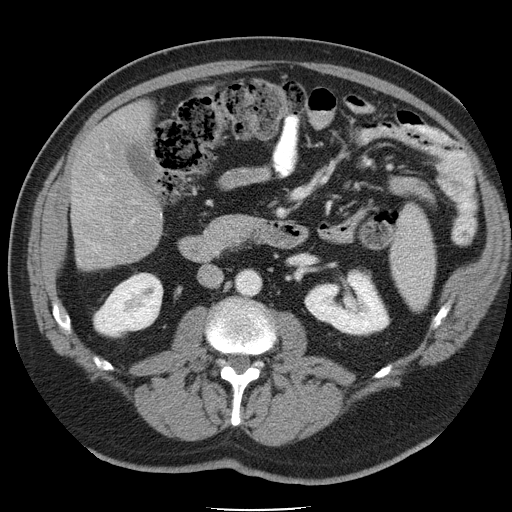
Contrast-enhanced abdominal CT, one axial slice. Slice 14 of 45 in the series (ordered by position). 120 kVp. Intravenous contrast given. Soft-tissue window (W 400 / L 40 HU). 5 mm slice thickness. 512 × 512 image matrix, field of view 386 × 386 mm. Male patient, age 65 years. Case-level facts recorded for this patient, not image findings: diagnosis: colorectal cancer liver metastases, imaged before liver resection; multiple liver metastases: yes; largest metastasis: 4.9 cm; disease in both lobes: no.
Structures marked on this image (outlined manually by an expert reader):
- liver: bounding box <72,107,163,269> (left, top, right, bottom; pixels)
- planned liver remnant (the part of the liver to remain after resection): <92,107,146,161>